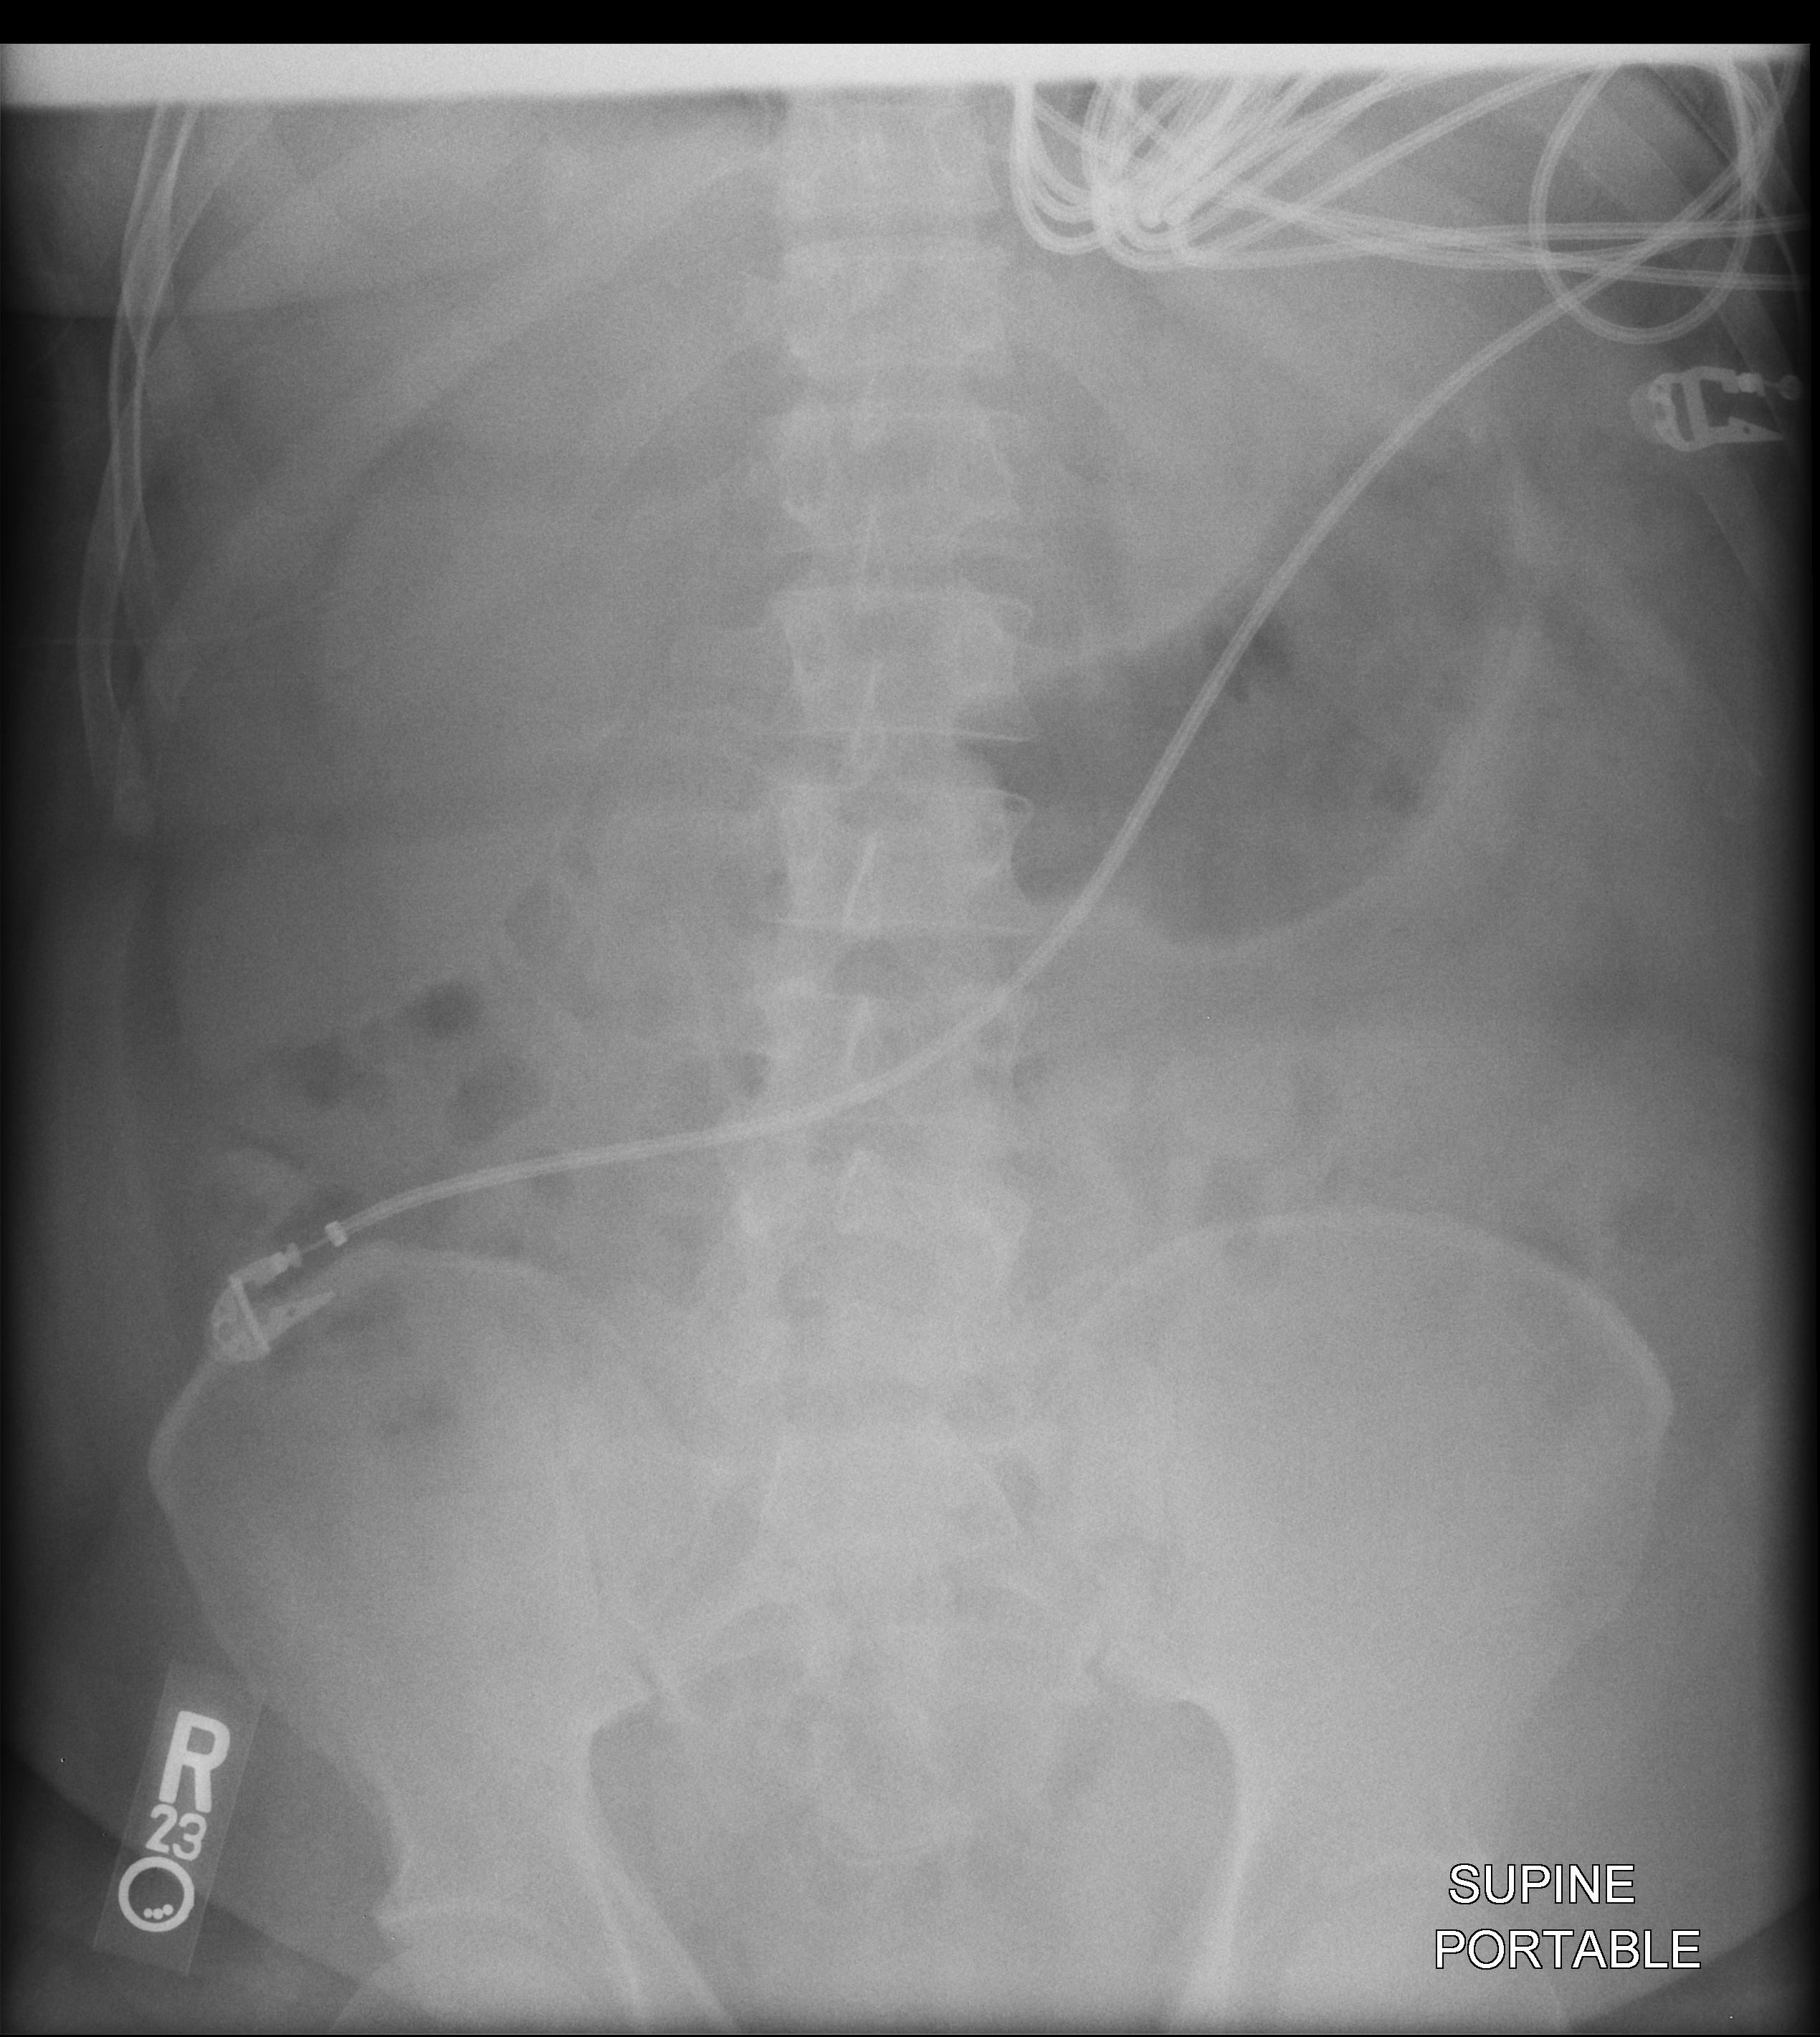
Bedside abdomen radiograph (computed radiography), anteroposterior (AP) projection. Male patient hospitalised with COVID-19, age 18–59 years.
Hospital-stay facts (about this admission, not read from this image; timing relative to this image not recorded):
- COPD (admission record): yes
- diabetes (admission record): no